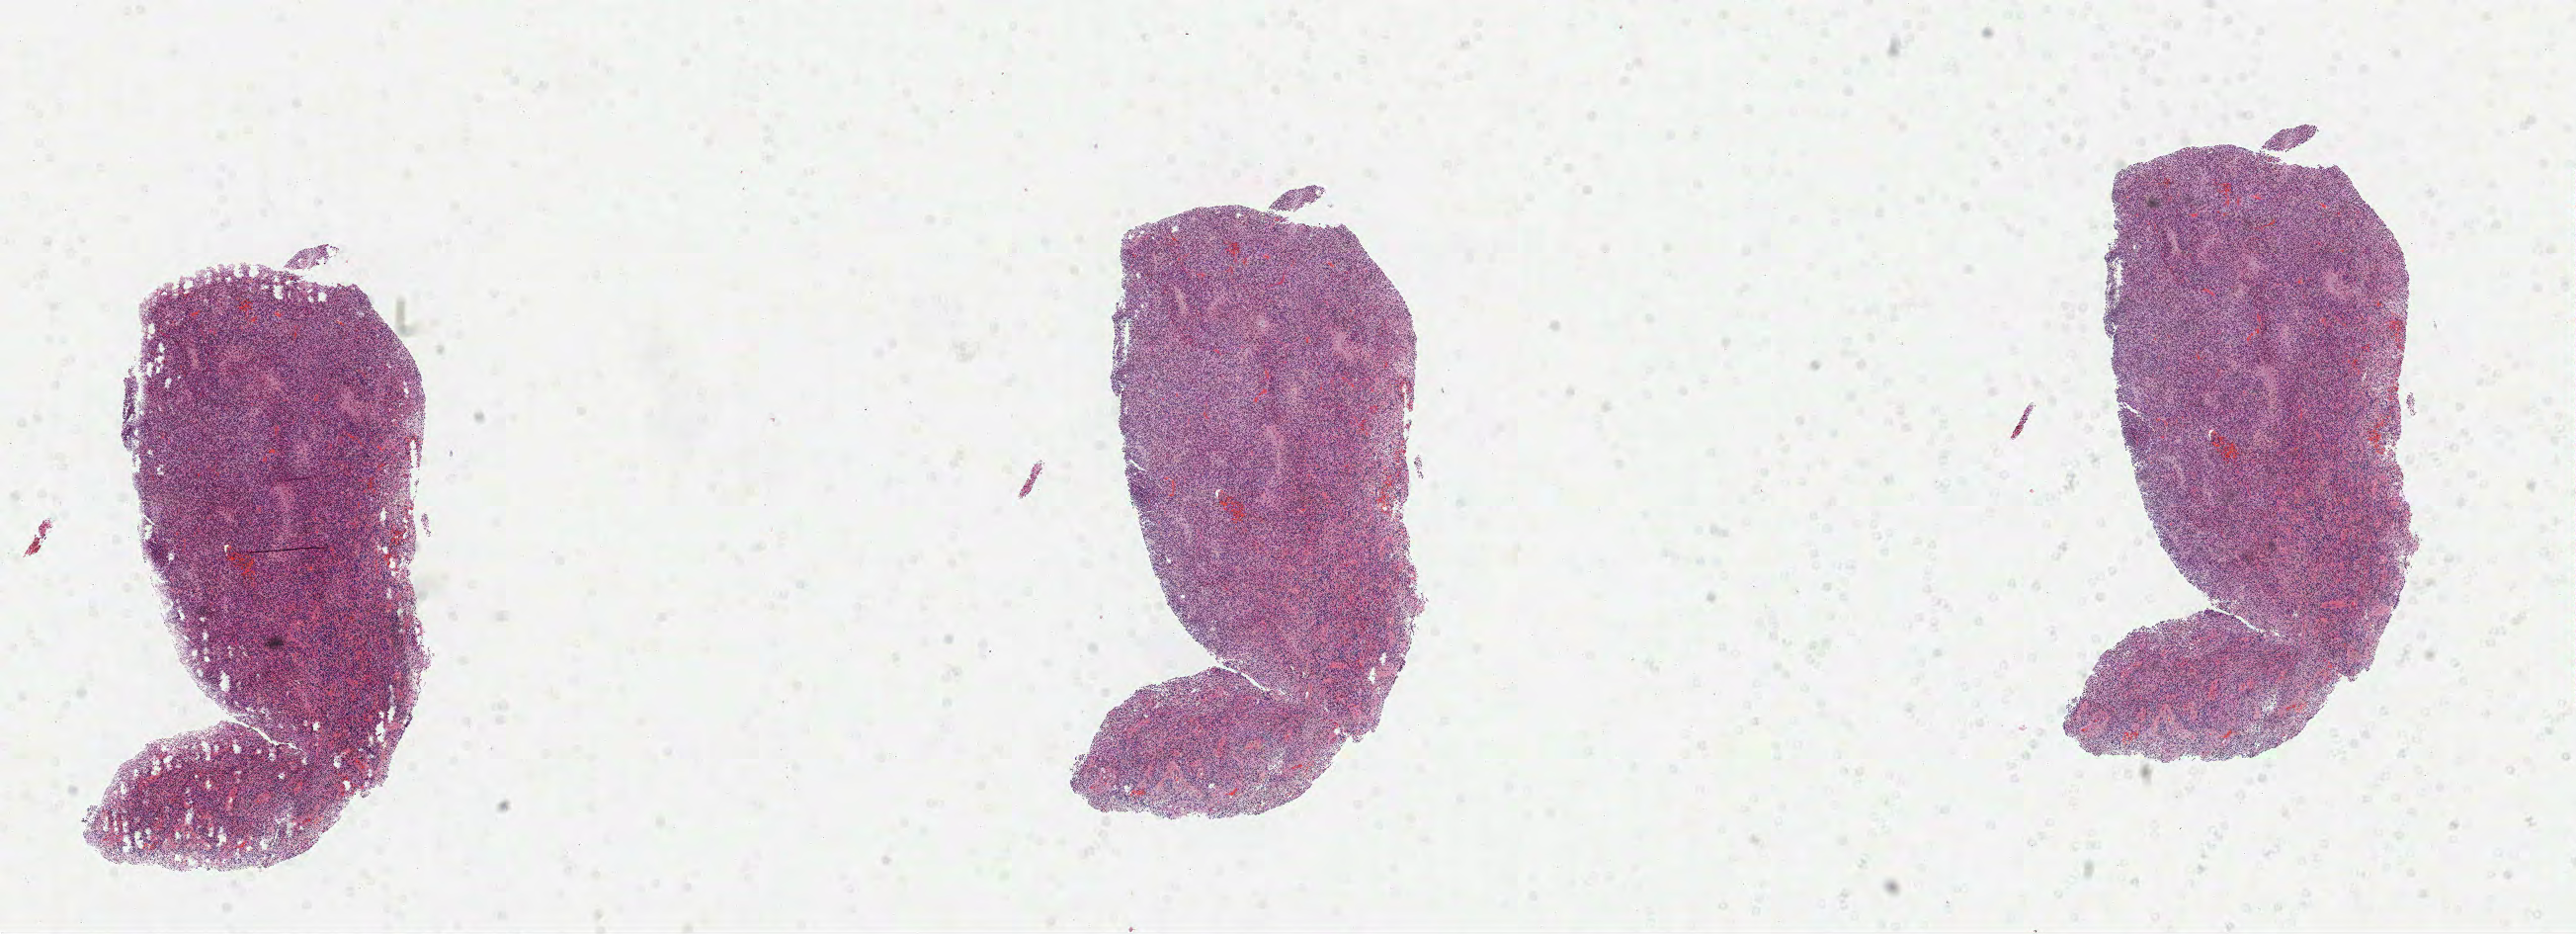
Whole-slide histology image, H&E — shown as a low-resolution overview of the whole scanned area (about 21.0 x 7.6 mm, slide scanned at 40x). Formalin-fixed paraffin-embedded (FFPE) diagnostic section. Brain, primary tumour sample. Female patient; age at initial diagnosis 54 years.
- diagnosis: Glioblastoma